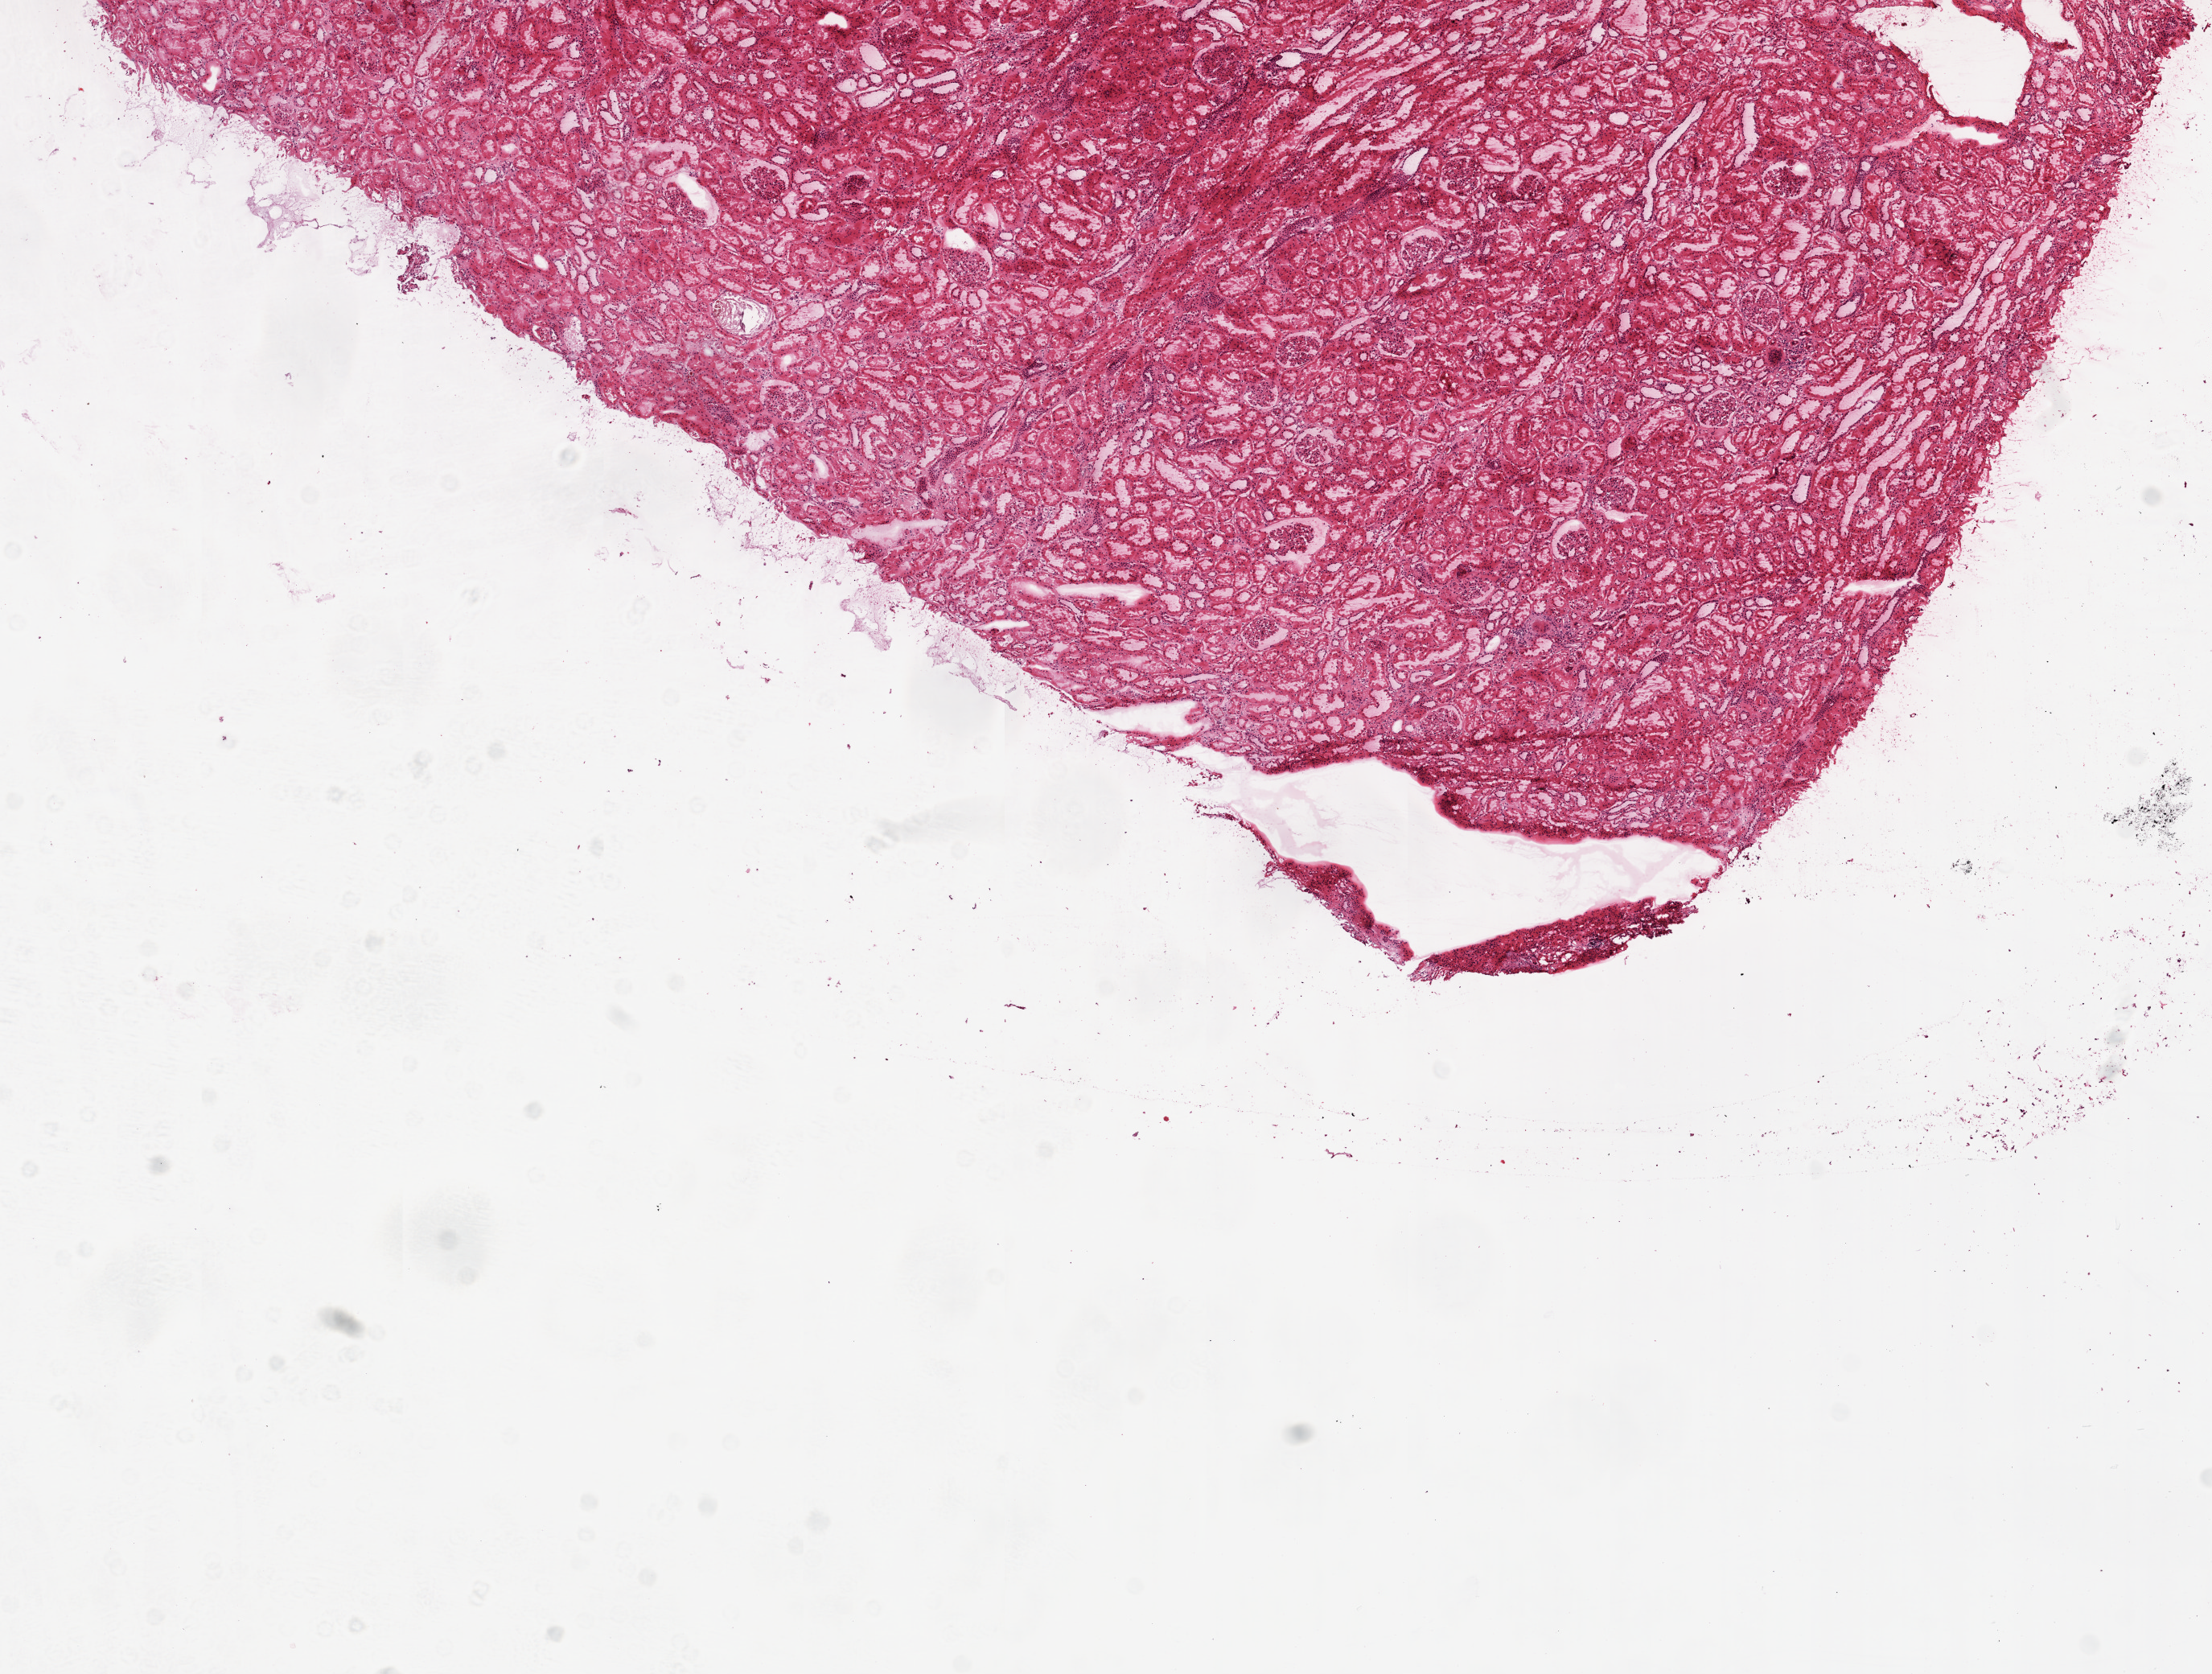
H&E-stained whole-slide image — shown as a low-resolution overview of the whole scanned area (about 11.0 x 8.3 mm, acquisition: 20x scan); frozen section from the top of the tissue portion; sample: solid tissue normal (non-tumour tissue), kidney. Female, age 65 years at initial diagnosis.
This section: solid tissue normal (non-tumour) sample from the same patient. Patient diagnosis: Clear cell adenocarcinoma, NOS.